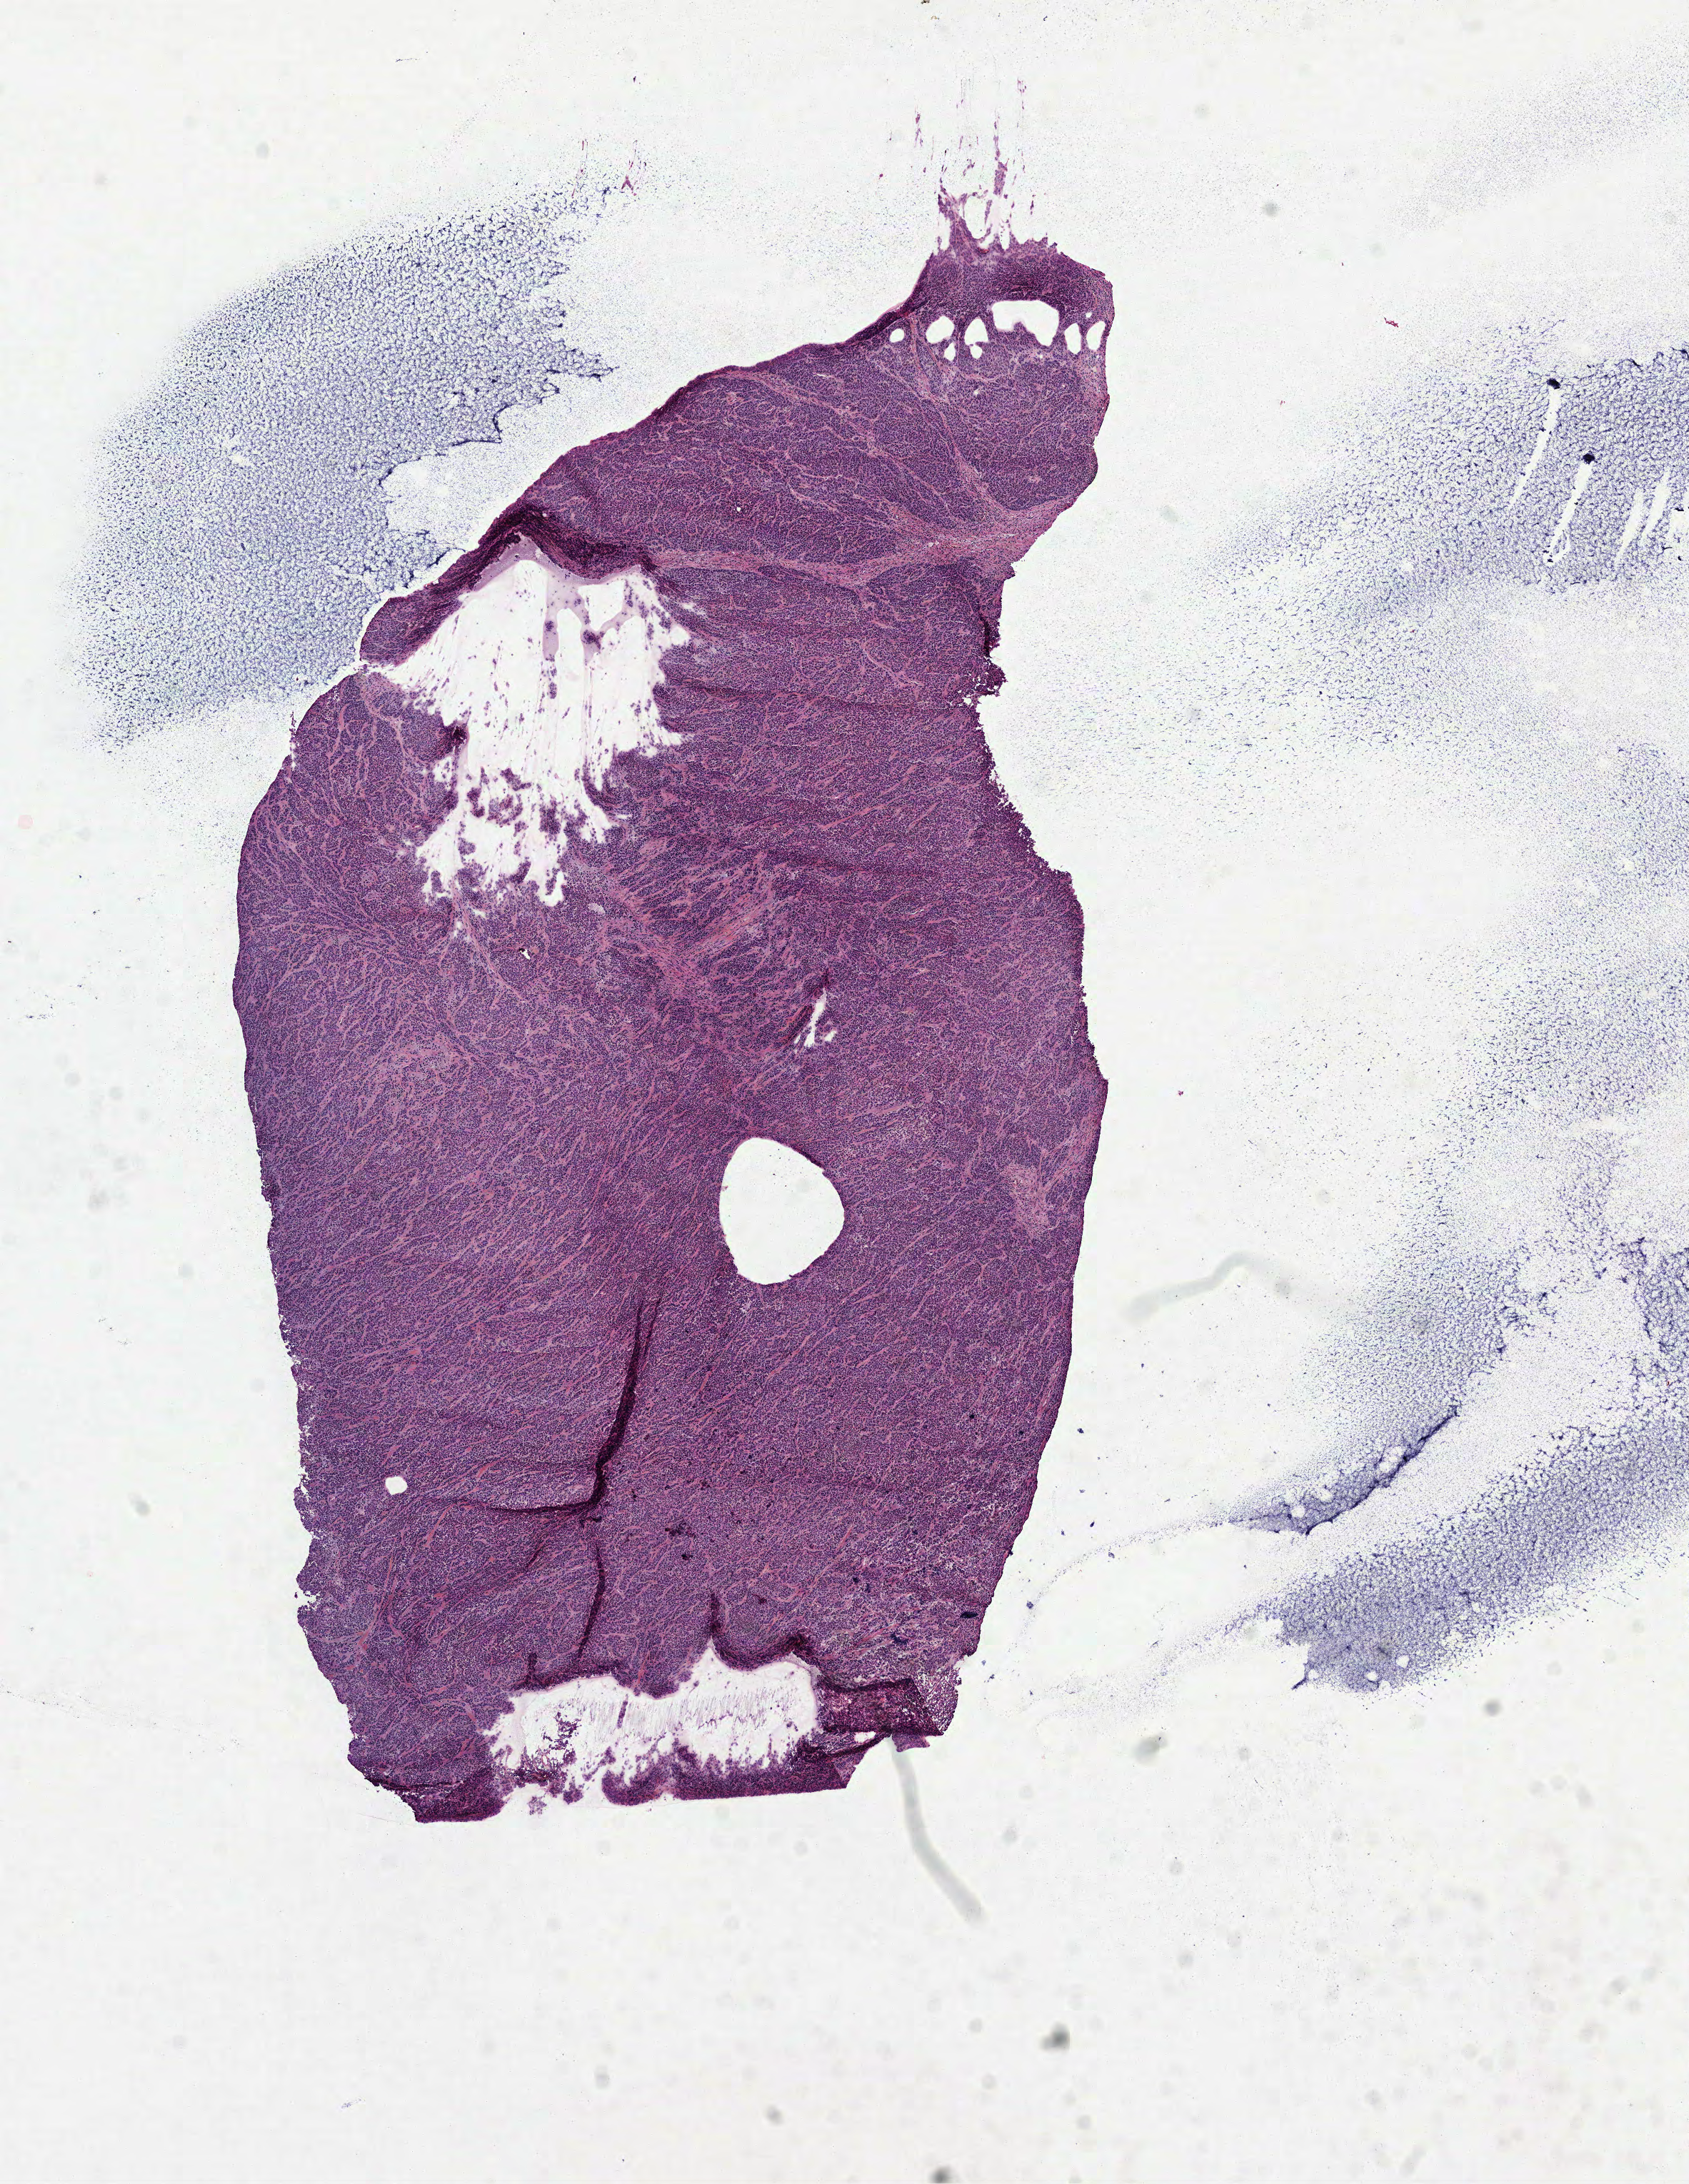
Whole-slide histology image, H&E-stained — a low-resolution overview of the entire scanned area, about 9.5 x 12.3 mm, frozen section from the top of the tissue portion, primary tumour sample from the colon. Female patient; age at initial diagnosis 84 years. Pathologist review of this section (percent, as recorded): tumour cells 90%, tumour nuclei 90%, normal cells 0%, stromal cells 10%, necrosis 0%.
- AJCC pathologic stage: IIB
- pathologic diagnosis: Adenocarcinoma, NOS (cecum)
- TNM: T4b N0 MX